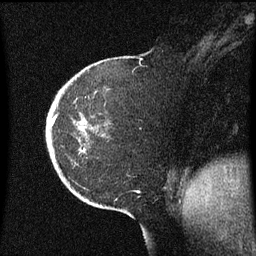
Breast MRI (dynamic contrast-enhanced), one sagittal slice; slice 16 of 60 in the series (ordered by position); dynamic contrast-enhanced series, image 2 of 3 at this slice position (ordered by acquisition); 1.5 T; TE 4.2 ms, TR 8.4 ms; 2 mm slice thickness; 256 × 256 image matrix, field of view 200 × 200 mm. Patient: female, 38 years. From the clinical record (not read from this slice): setting: breast cancer imaged before/during neoadjuvant chemotherapy; receptor status: HER2-positive.
Outlined on this slice (semi-automatic segmentation, software-assisted and operator-edited):
- analysis volume of interest (the breast-tissue region the enhancement analysis was run in; not a lesion): box from (x=47, y=56) to (x=137, y=185) px
- tumour enhancement mask (voxels above the 70 % enhancement threshold inside the analysis volume of interest): (x=53, y=118)–(x=55, y=123)